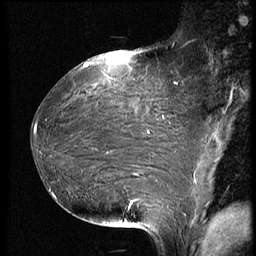
Breast MRI (dynamic contrast-enhanced), one sagittal slice. Position 32 of 66 along the scan axis. Dynamic contrast-enhanced series, image 2 of 3 at this slice position (ordered by acquisition). 1.5 T. TE 4.2 ms, TR 8.9 ms. 256 × 256 image matrix. Female patient, age 39 years. Case-level facts recorded for this patient, not image findings: setting: breast cancer imaged before/during neoadjuvant chemotherapy; receptor status: HER2-positive.
Outlined on this slice (semi-automatic segmentation, software-assisted and operator-edited):
- analysis volume of interest (the breast-tissue region the enhancement analysis was run in; not a lesion): box from (x=32, y=75) to (x=188, y=218) px
- tumour enhancement mask (voxels above the 140 % enhancement threshold inside the analysis volume of interest): (x=34, y=125)–(x=141, y=204)